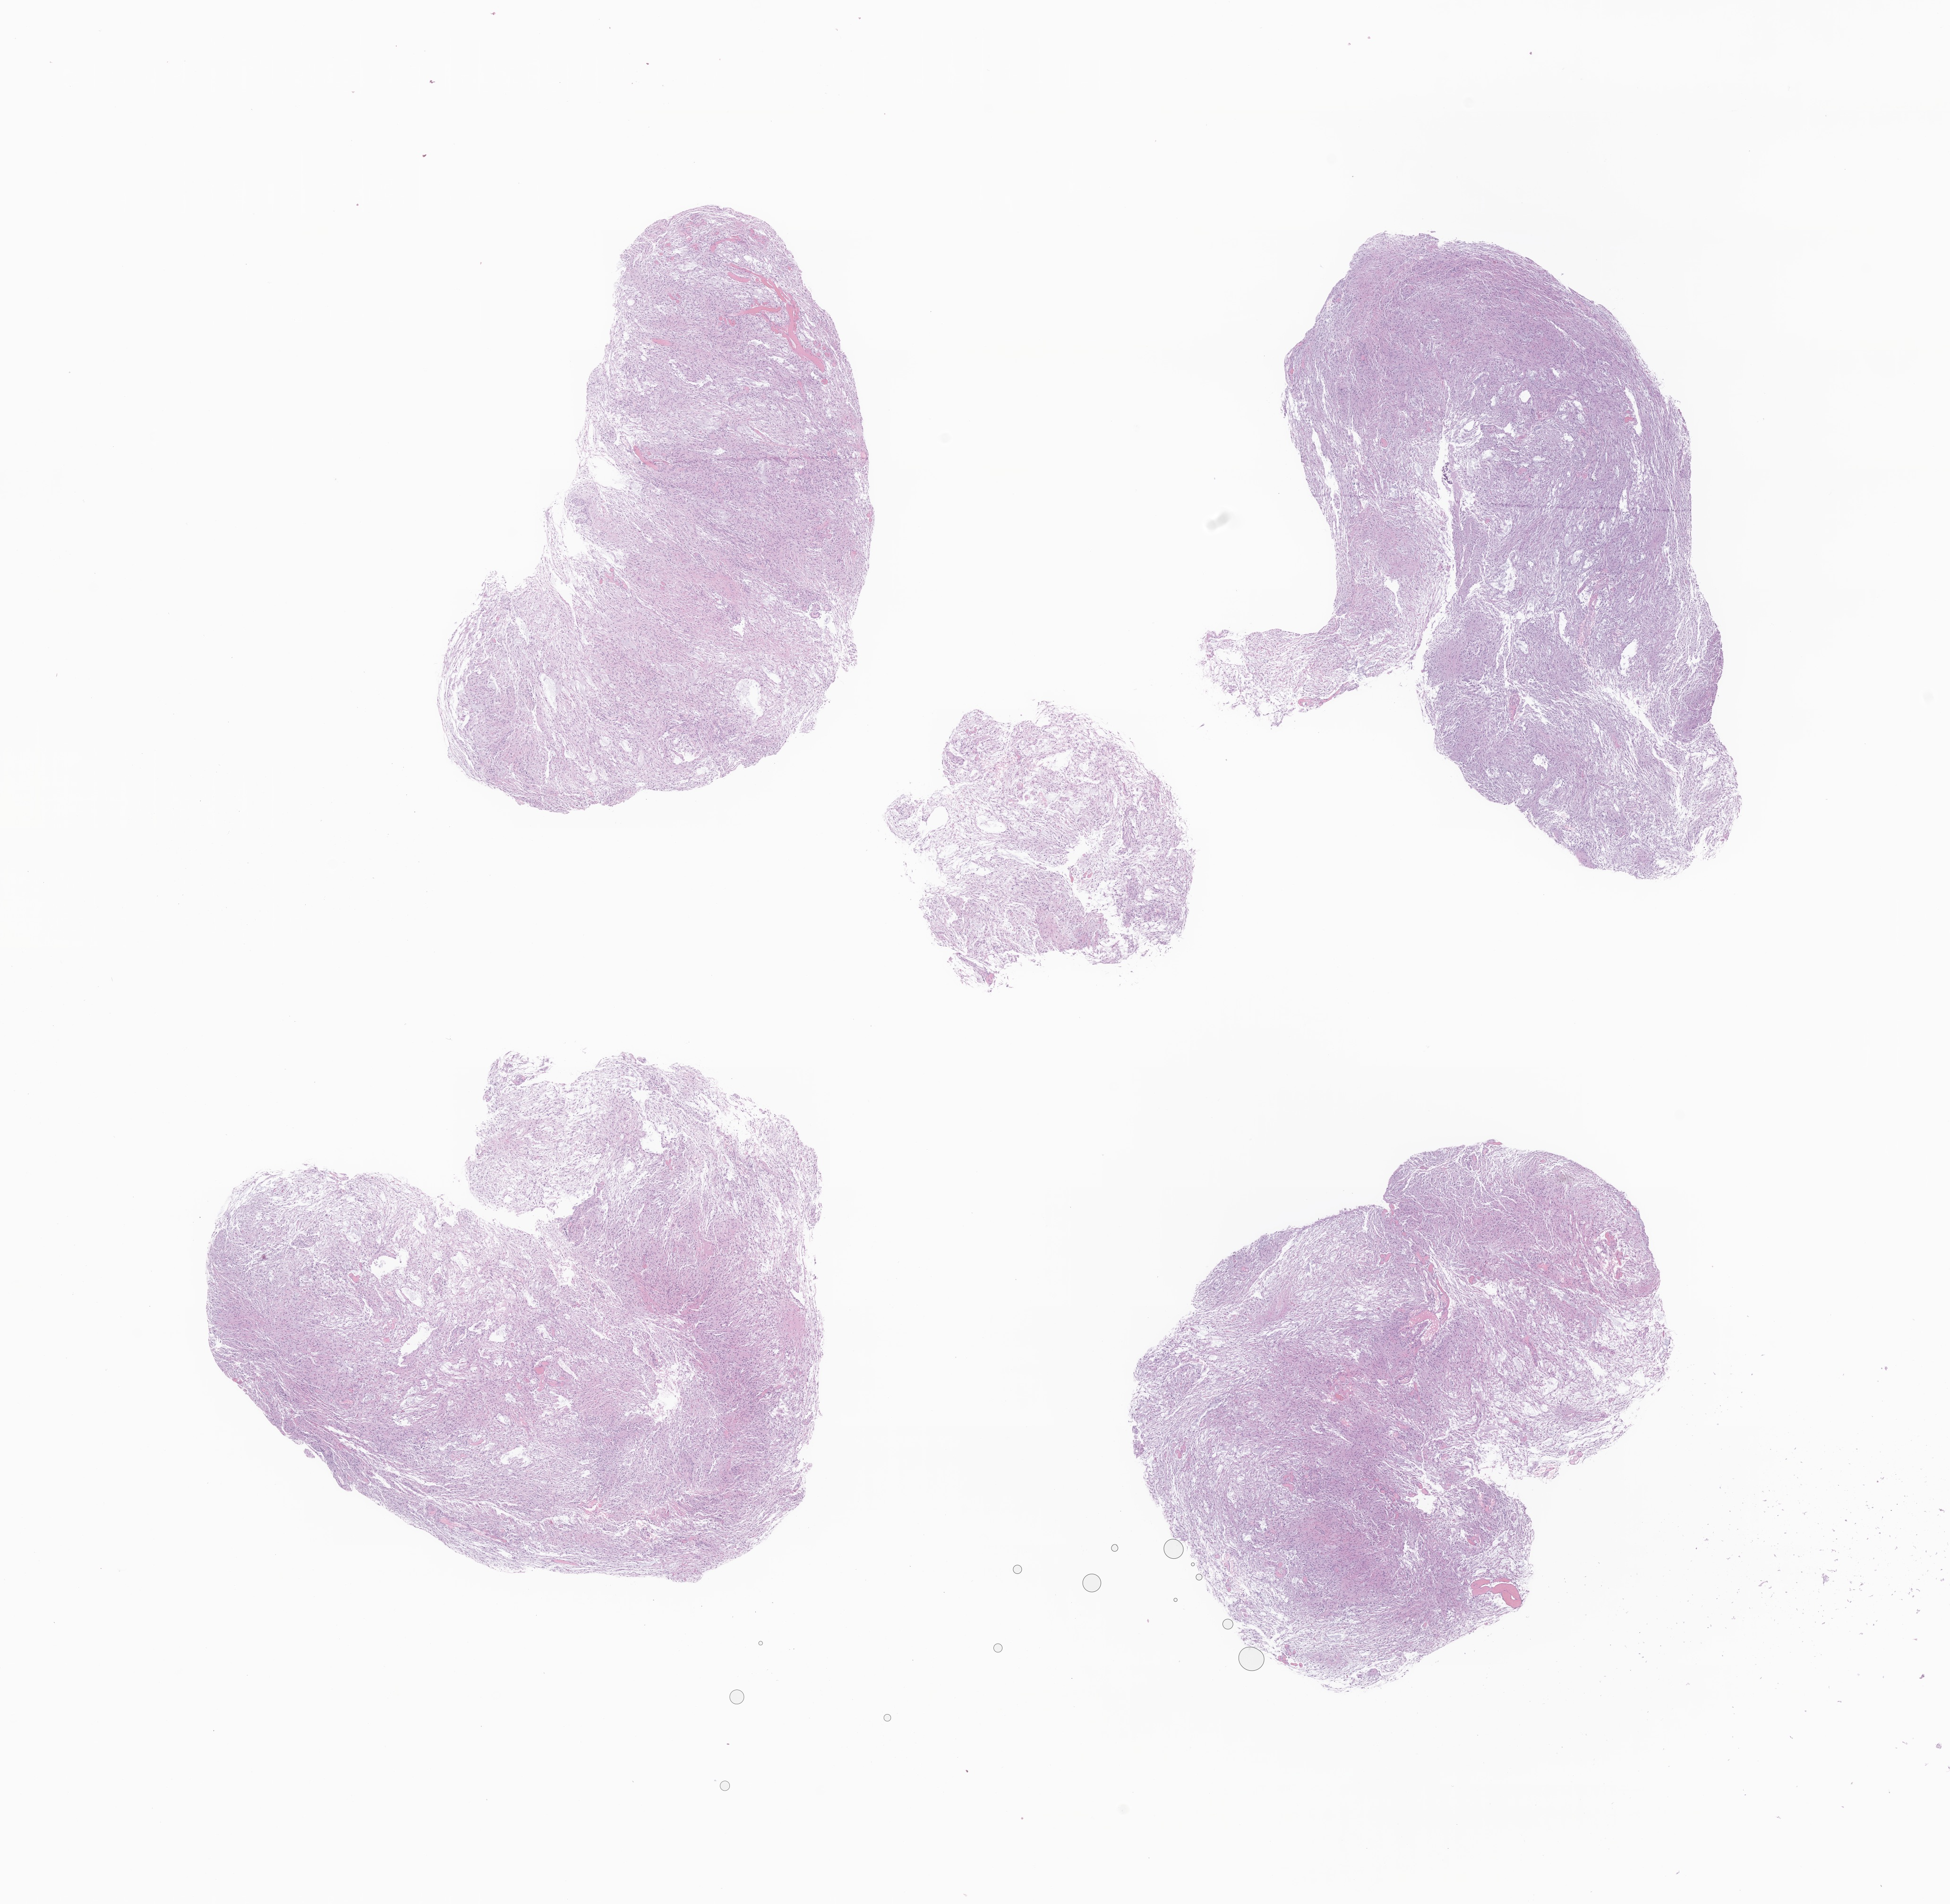
Whole-slide image, hematoxylin and eosin (H&E) stain of tumor tissue from the brain, a low-resolution overview of the entire scanned area, about 17.4 x 17.0 mm, formalin-fixed paraffin-embedded section. Patient female; age 116 months (9 years 8 months).
- recorded diagnosis: Neoplasm, uncertain whether benign or malignant